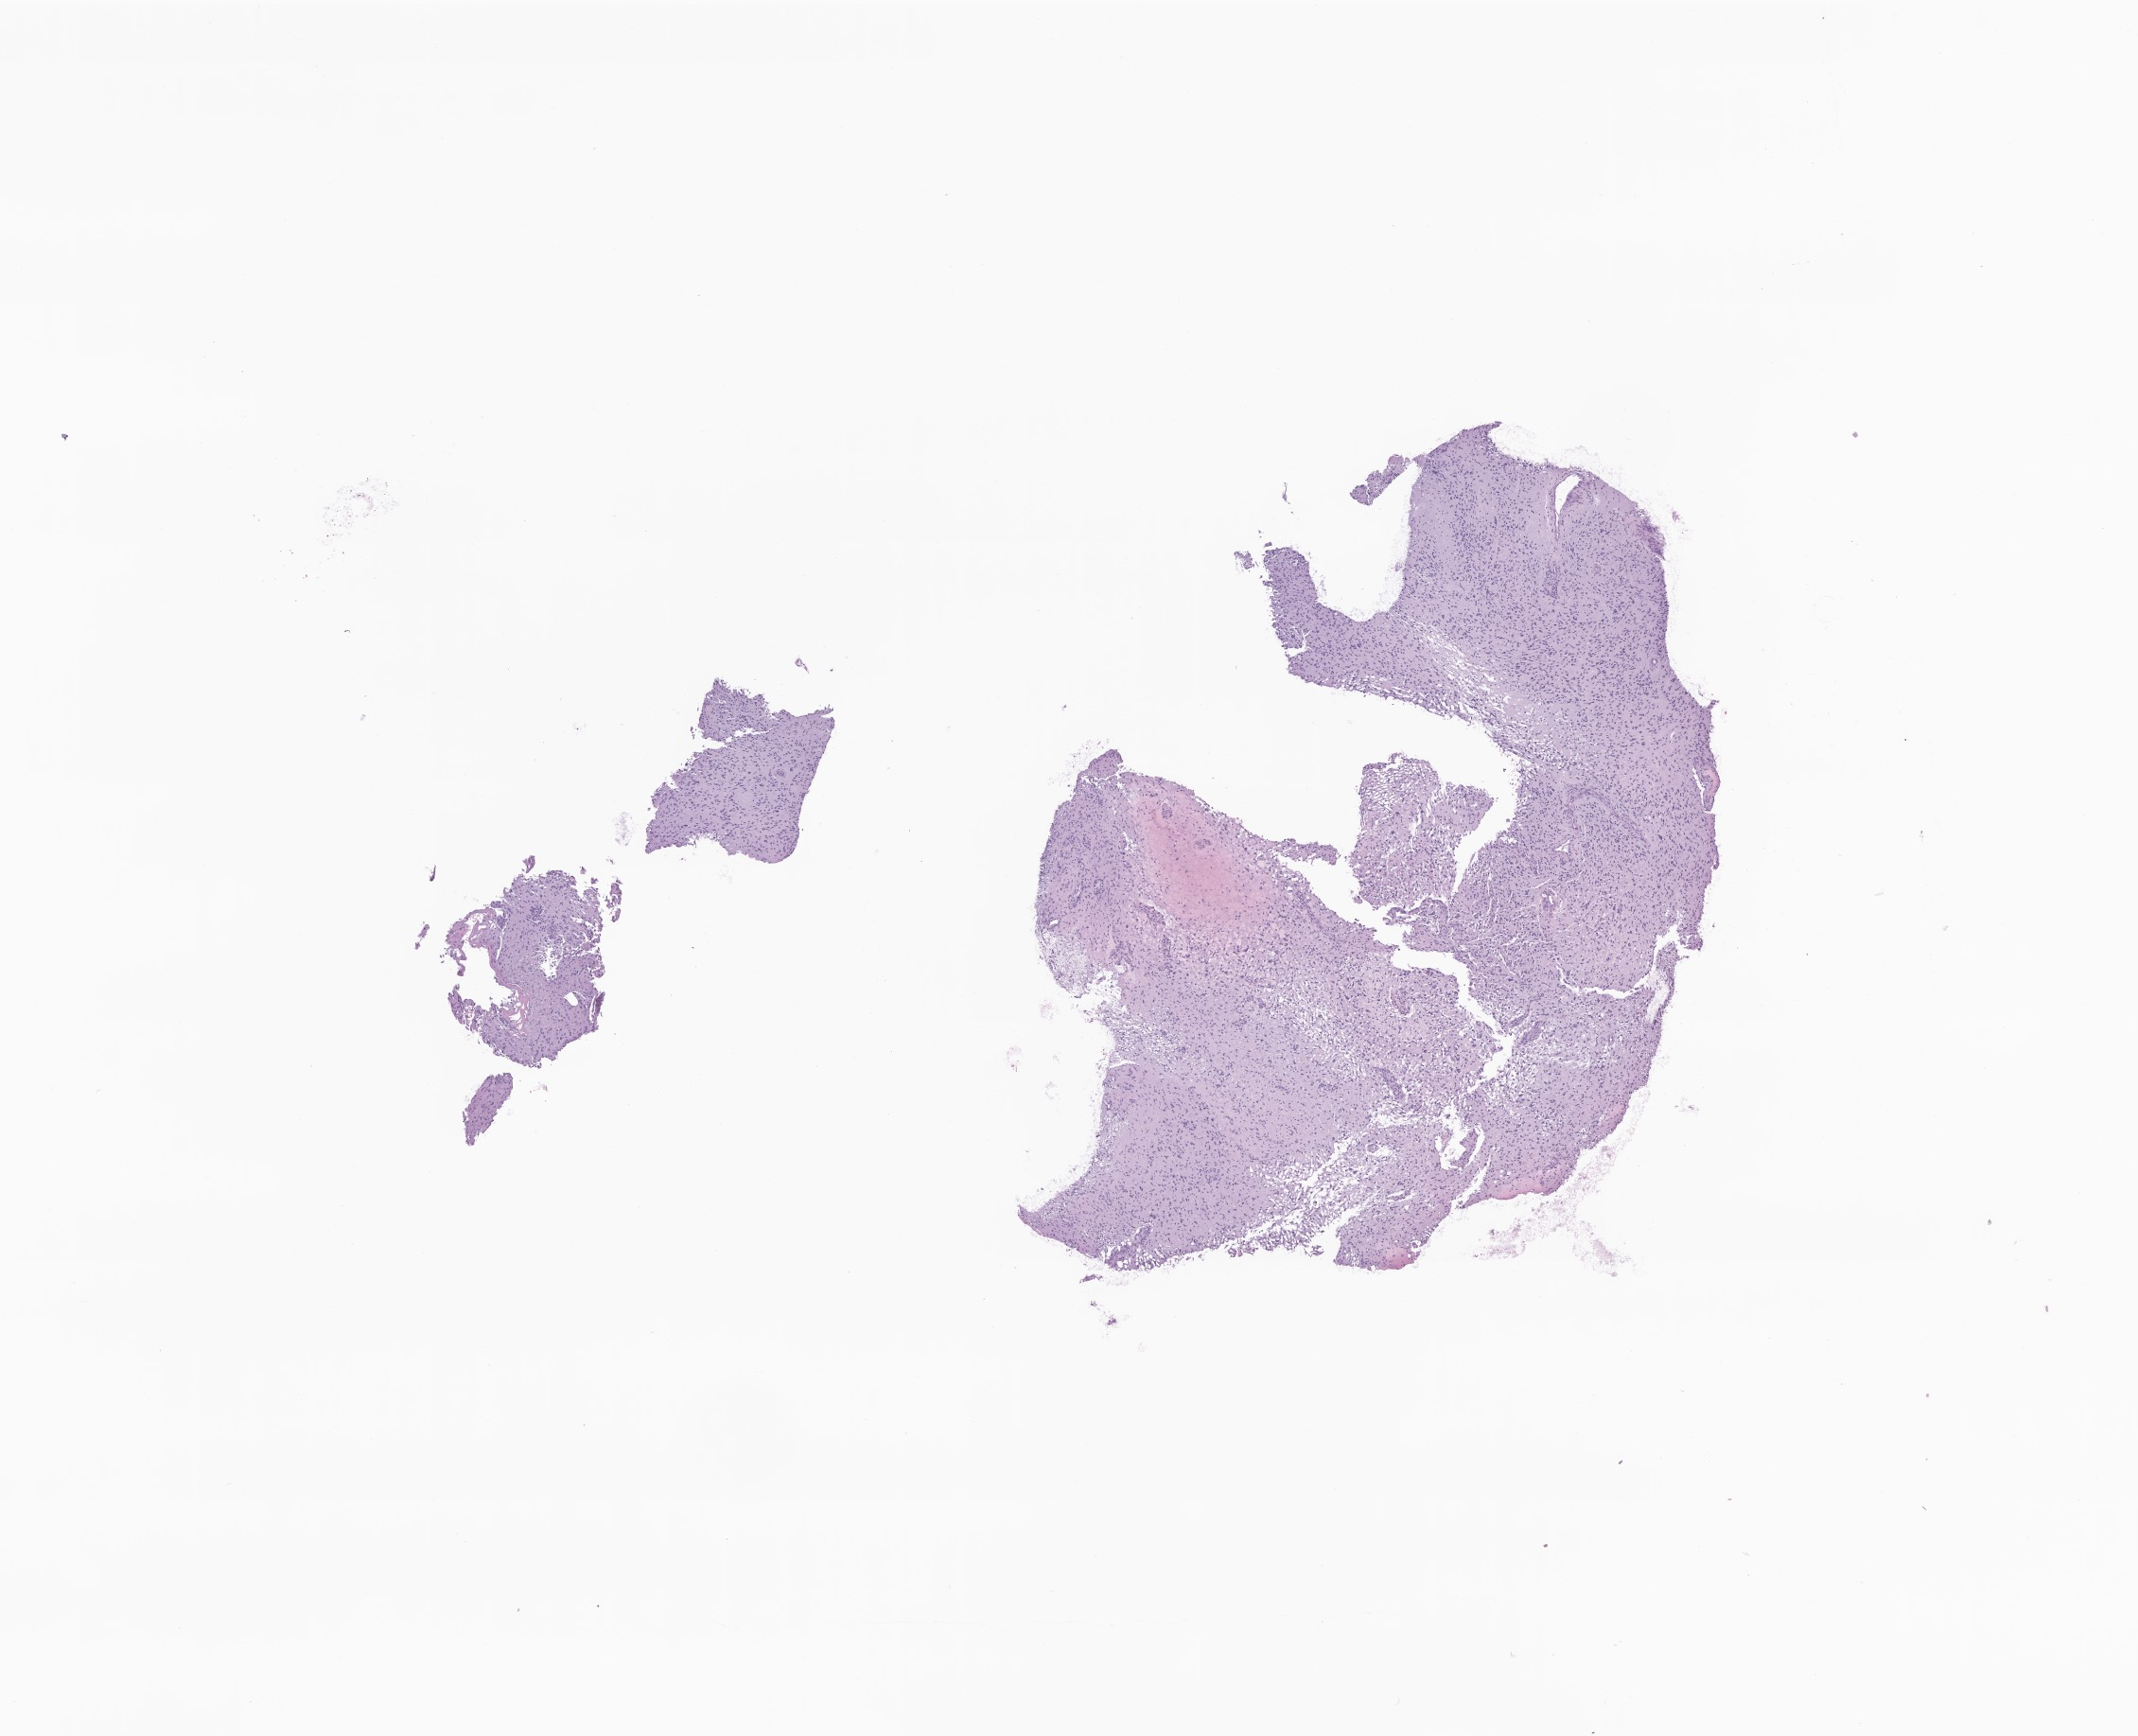
Whole-slide image, hematoxylin and eosin (H&E) stain of tumor tissue from the cerebellum, whole scanned area (about 9.5 x 7.7 mm) shown as a low-resolution overview, formalin-fixed paraffin-embedded section. Patient male; age 115 months (9 years 7 months).
Diagnosis (ICD-O-3 morphology term): Astrocytoma, NOS.